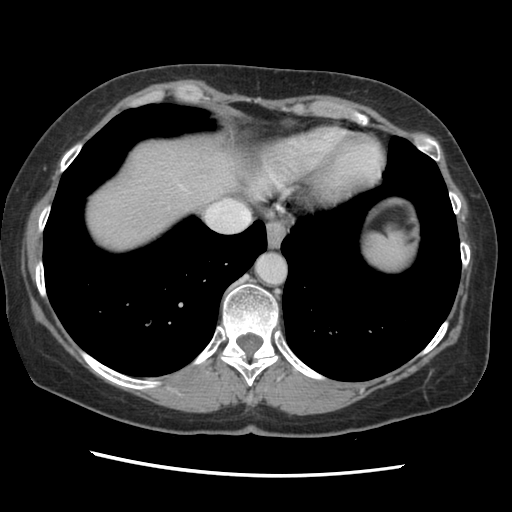
Contrast-enhanced abdominal CT, one axial slice. Slice 123 of 141 in the series (ordered by position). Soft-tissue window (W 400 / L 40 HU). 2.5 mm slice thickness. 512 × 512 image matrix. Female patient, age 61 years. From the clinical record (not read from this slice): diagnosis: colorectal cancer liver metastases, imaged before liver resection; multiple liver metastases: no; largest metastasis: 2.4 cm; chemotherapy before resection: no.
Structures marked on this image (manually delineated by an expert):
- hepatic veins: bounding box [x1, y1, x2, y2] px = [210, 200, 226, 207]
- liver: [85, 139, 239, 250]
- planned liver remnant (the part of the liver to remain after resection): [85, 139, 239, 250]